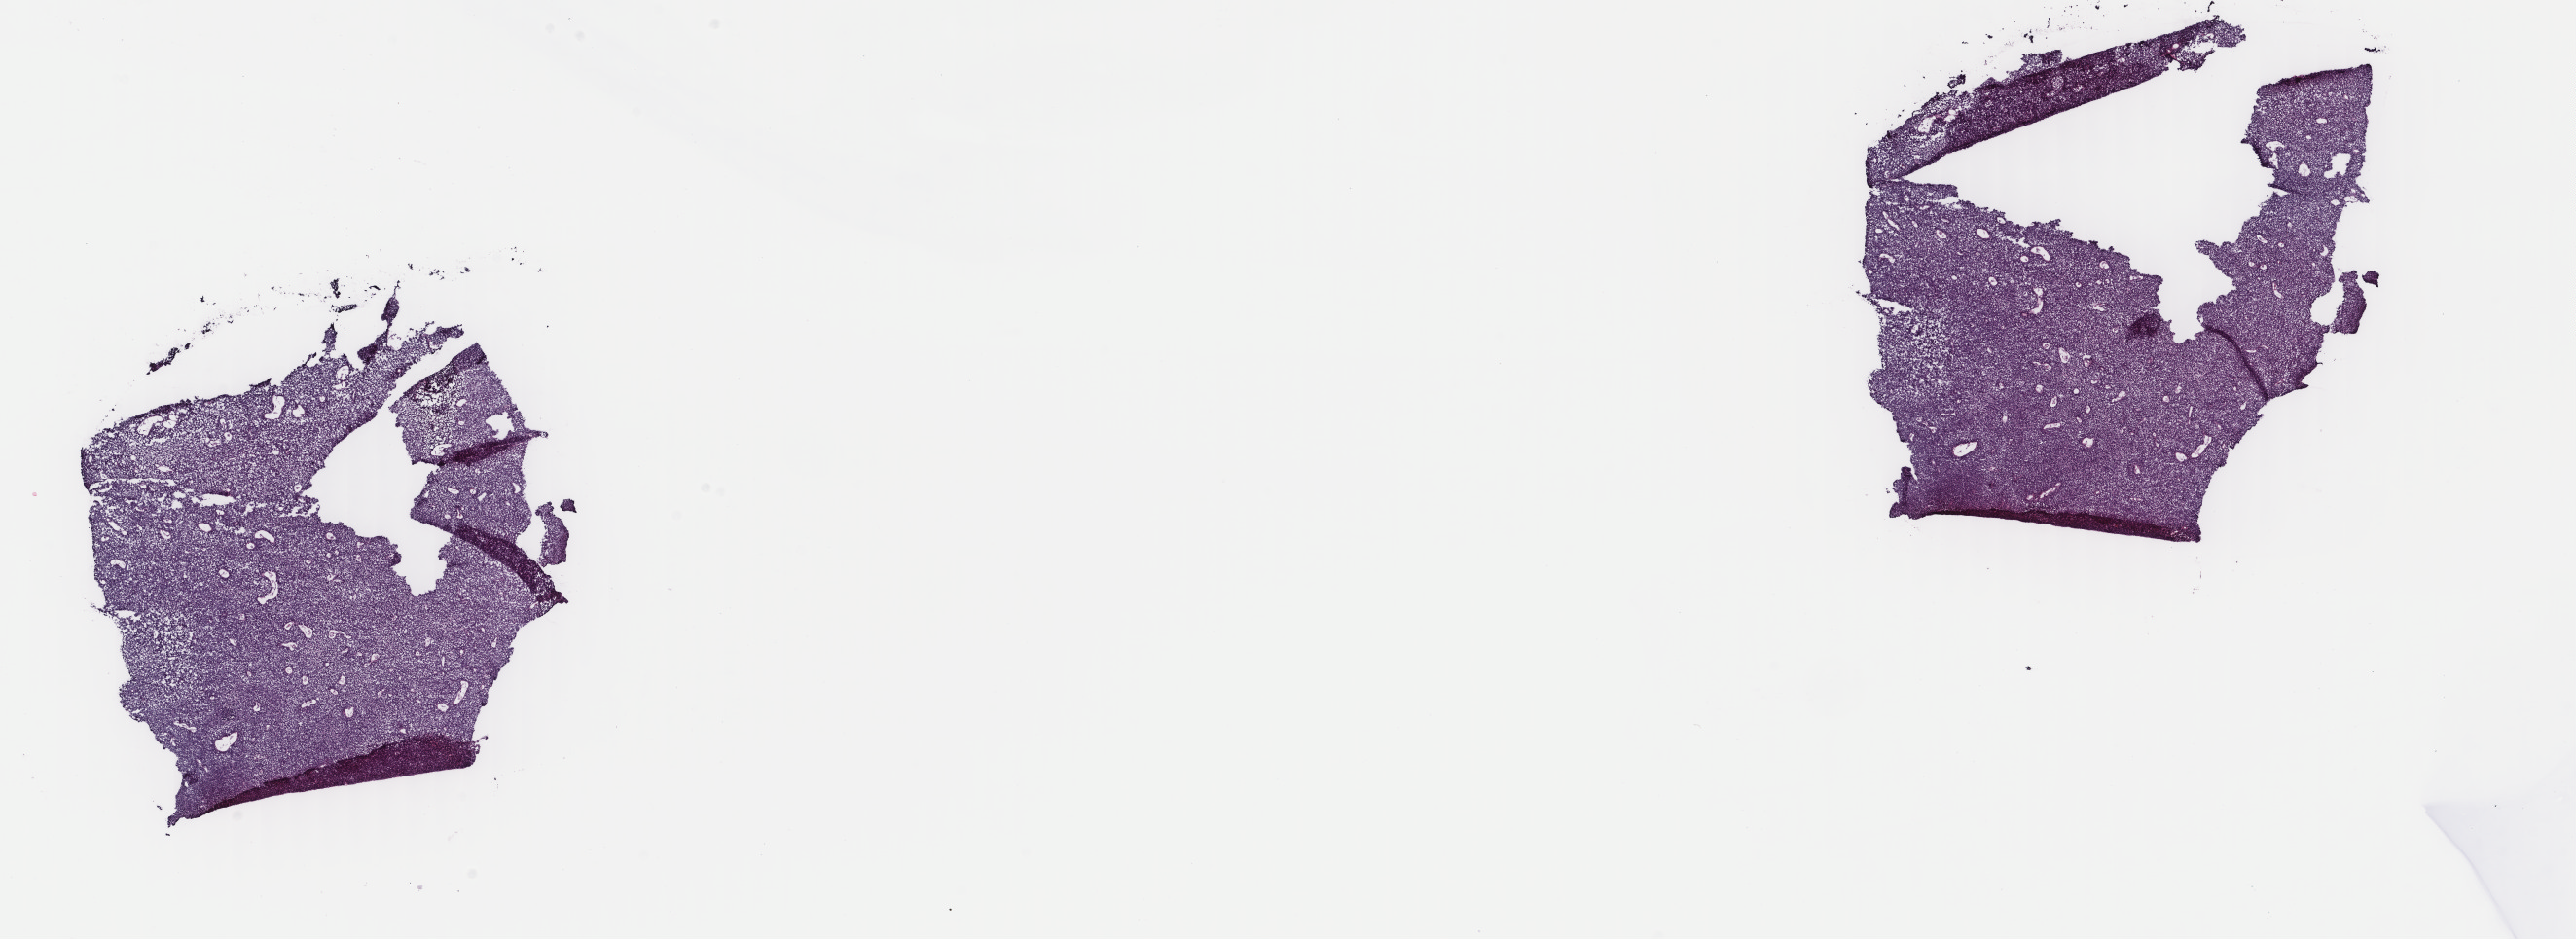
Whole-slide histology image, H&E, shown as a low-resolution overview of the whole scanned area (about 21.0 x 7.7 mm, acquisition: 40x scan), frozen section from the top of the tissue portion, metastatic tumour sample, sampled site: peritoneum. Patient: male, age at initial diagnosis 25 years. Slide review estimates, as recorded: tumour cells 100%, tumour nuclei 99%, normal cells 0%, stromal cells 0%, necrosis 0%. Inflammatory infiltration, as recorded: lymphocyte infiltration 0%, monocyte infiltration 0%, neutrophil infiltration 0%.
- this section: metastatic tumour tissue
- patient diagnosis: Malignant melanoma, NOS